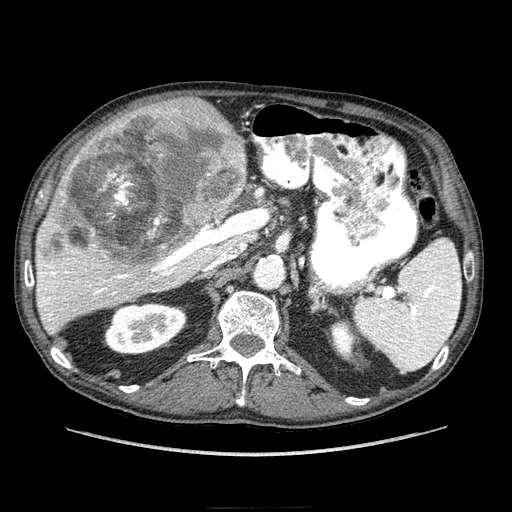
Contrast-enhanced abdominal CT (liver protocol), one axial slice; slice 143 of 218 in the series (ordered by position); reconstruction kernel STANDARD; 100 kVp; soft-tissue window (W 400 / L 40 HU); 2.5 mm slice thickness; 512 × 512 image matrix, field of view 380 × 380 mm. Case-level facts recorded for this patient, not image findings: diagnosis: hepatocellular carcinoma (patient treated with transarterial chemoembolisation; whether this scan precedes or follows treatment is not stated here); TNM stage (as recorded): Stage-IIIA; Child-Pugh class: A; tumour differentiation: well differentiated; tumour size: 20 cm.
Outlined on this slice (semi-automatically segmented with operator editing):
- liver parenchyma outside the tumour (the mass and vessels are separate outlines, so this box may not span the whole liver): bounding box <36,114,264,334> (left, top, right, bottom; pixels)
- mass: <37,96,246,276>
- liver vessels: <37,188,263,321>